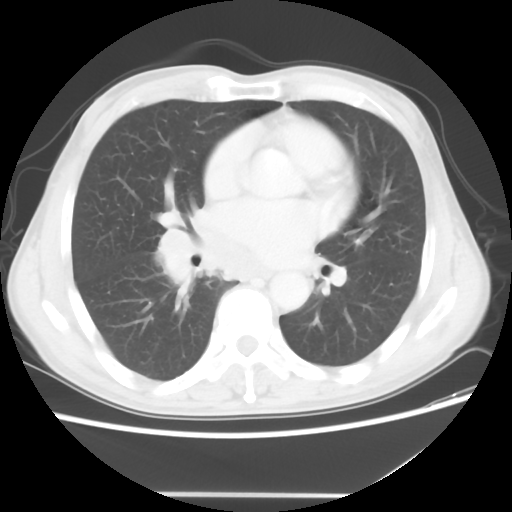
Chest CT, one axial slice; position 26 of 56 along the scan axis; reconstruction kernel STANDARD; 120 kVp; lung window (W 1500 / L -600 HU); 5 mm slice thickness; 512 × 512 image matrix, field of view 344 × 344 mm. Male patient, age 65 years. Case-level facts recorded for this patient, not image findings: clinical TNM (as recorded): T1c N3 M0.
Annotated regions visible in this slice (rectangle marked by the reading radiologist):
- lung tumour (recorded histology: small cell carcinoma): bounding box [x1, y1, x2, y2] px = [157, 221, 272, 295]